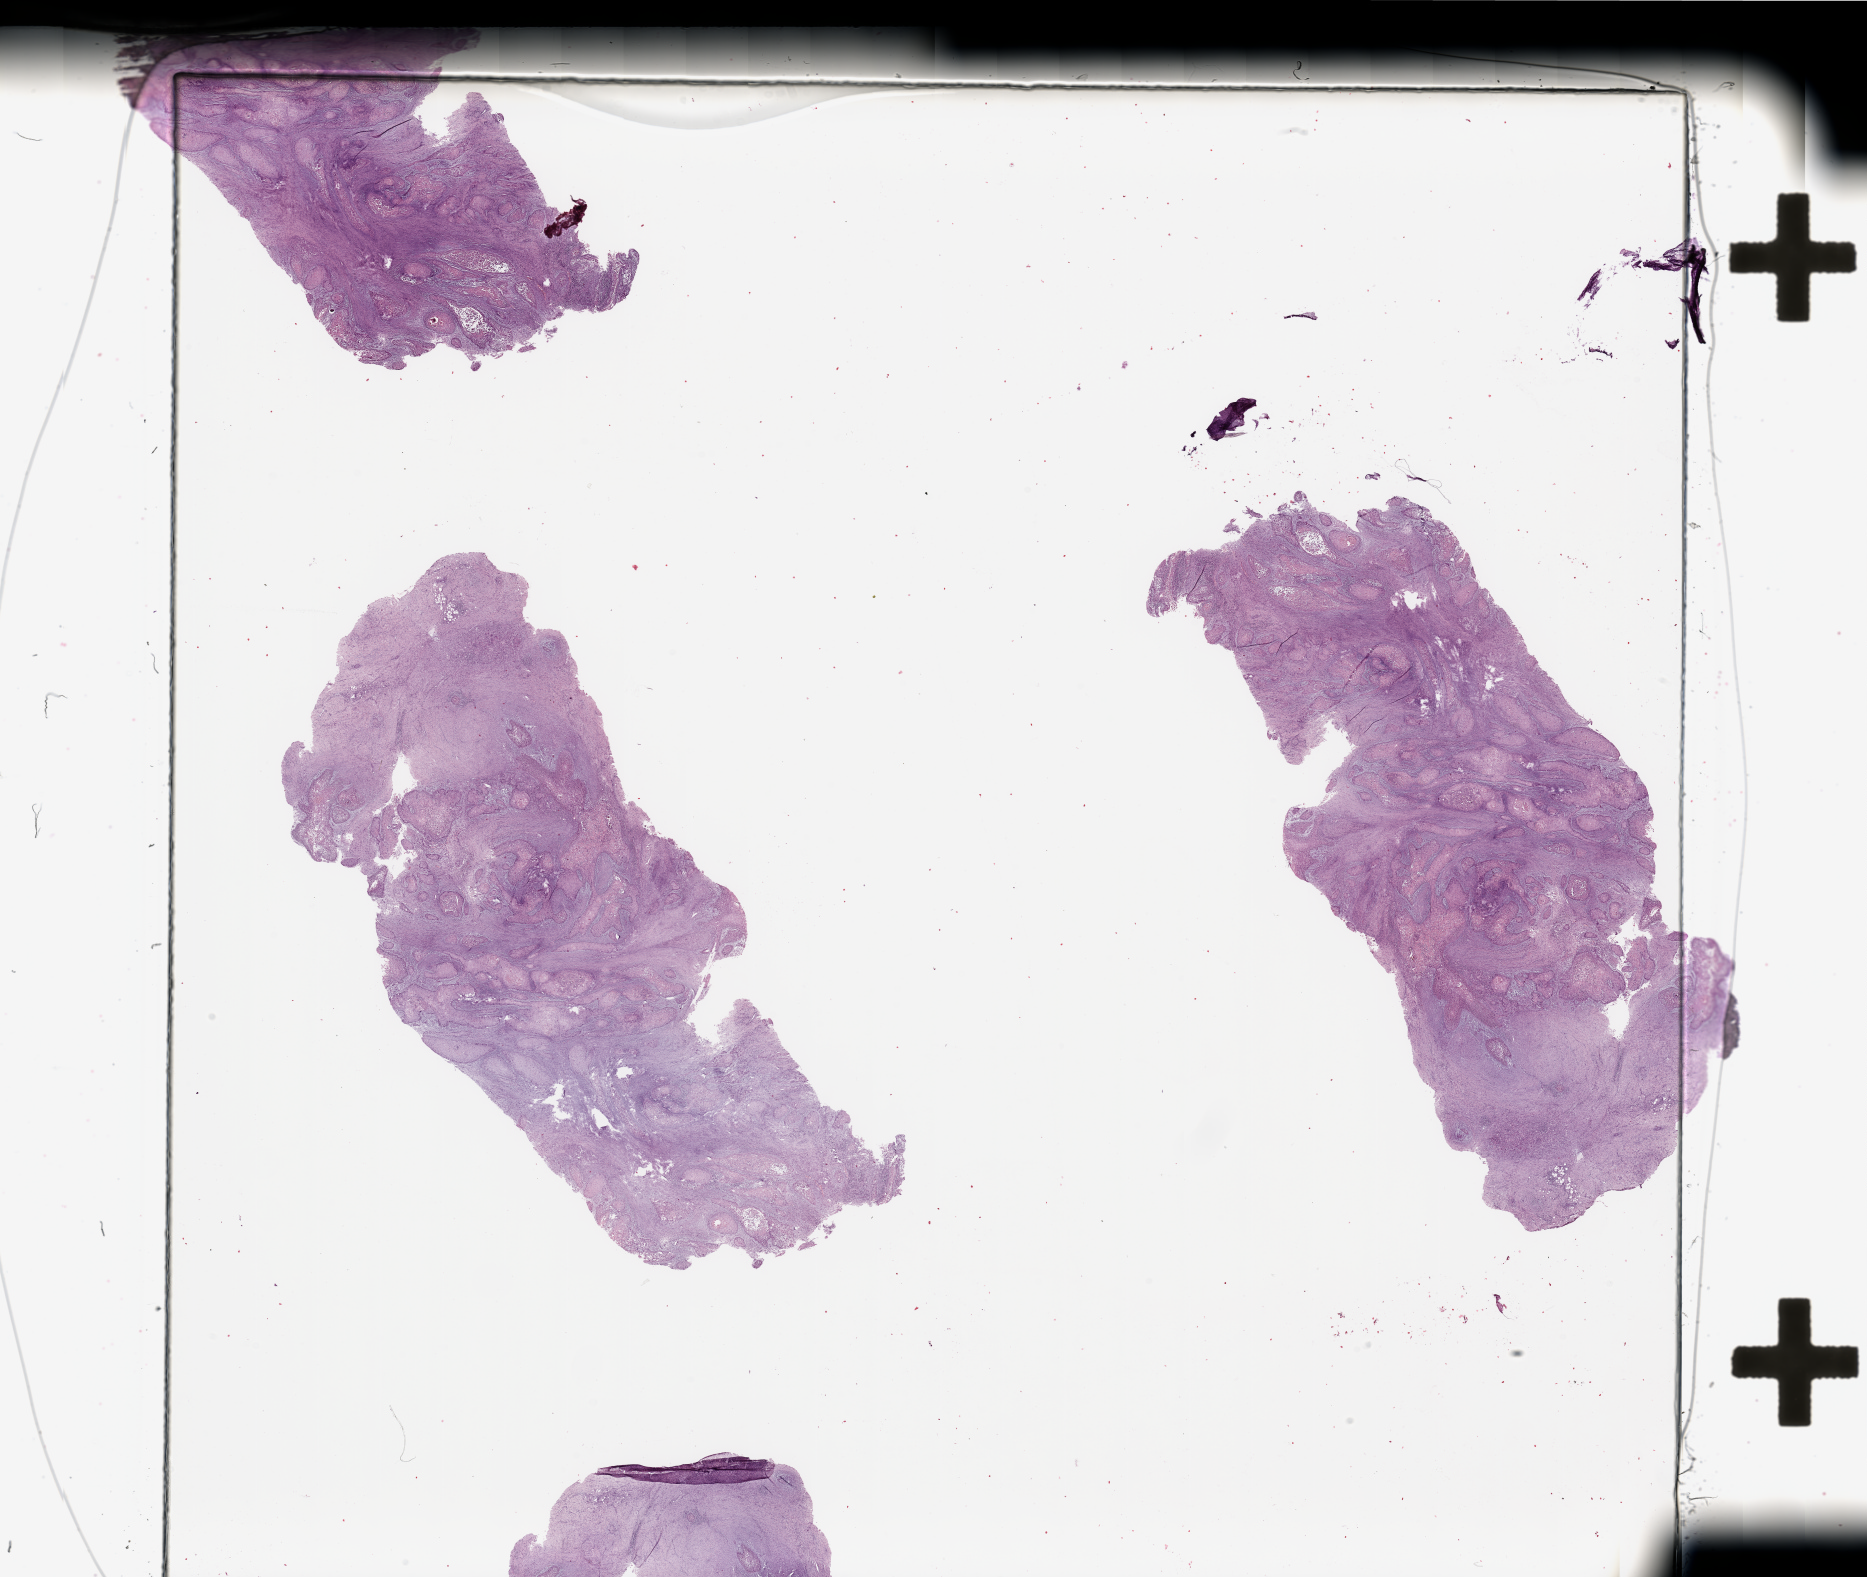
Whole-slide histology image, H&E — shown as a low-resolution overview of the whole scanned area (about 29.5 x 24.9 mm, acquisition: 20x scan); head and neck, tissue type not recorded. Patient: male, age 53 years.
Patient diagnosis: Squamous cell carcinoma, NOS.